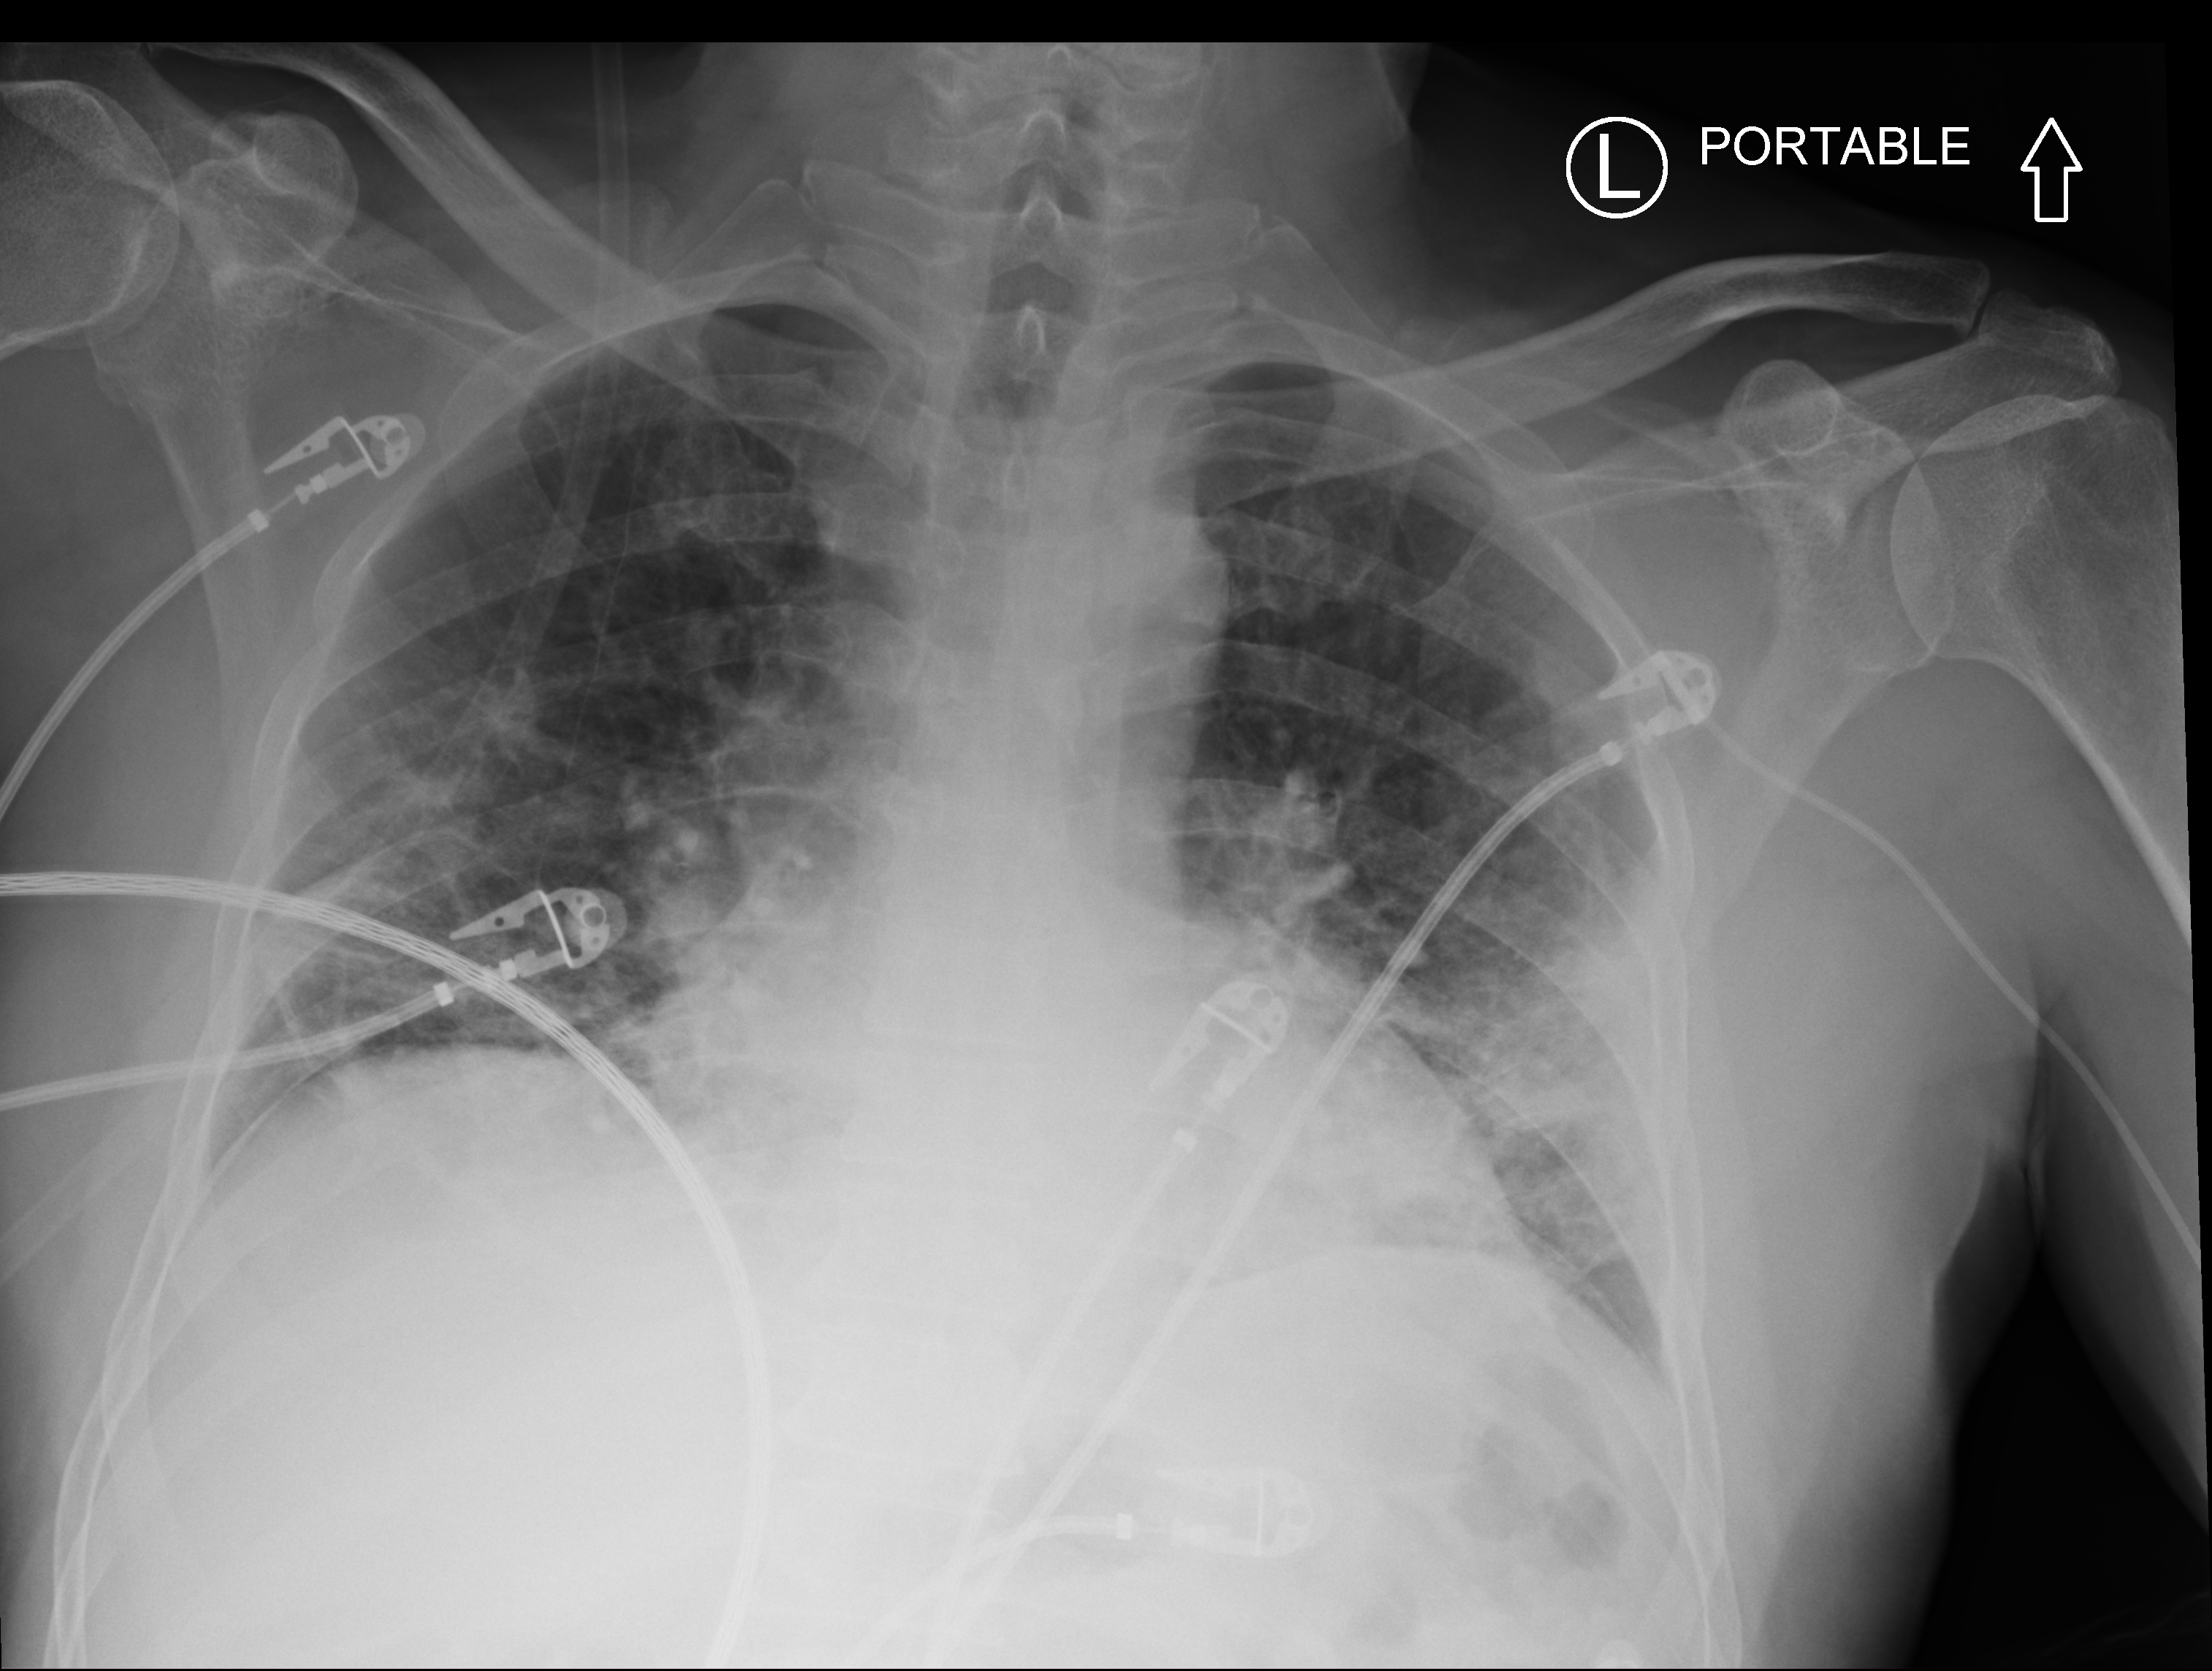
Portable chest radiograph; anteroposterior (AP) projection. Male patient hospitalised with COVID-19, age 18–59 years.
From the hospital-stay record, not from the radiograph (when in the stay this image was taken is not recorded): other chronic lung disease (admission record): no; COPD (admission record): no.